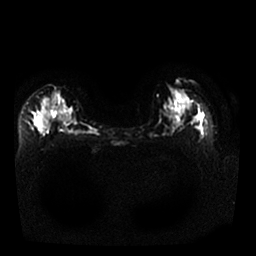
Breast MRI, one axial slice; slice 14 of 25 in the series (ordered by position); diffusion-weighted series; image 2 of 4 stored at this slice position (different b-values; order by instance number); 1.5 T; 4 mm slice thickness; 256 × 256 image matrix, field of view 340 × 340 mm. Female patient.
Outlined on this slice (outlined manually by an expert reader):
- tumour on diffusion-weighted imaging: bounding box [x1, y1, x2, y2] px = [42, 107, 64, 120]